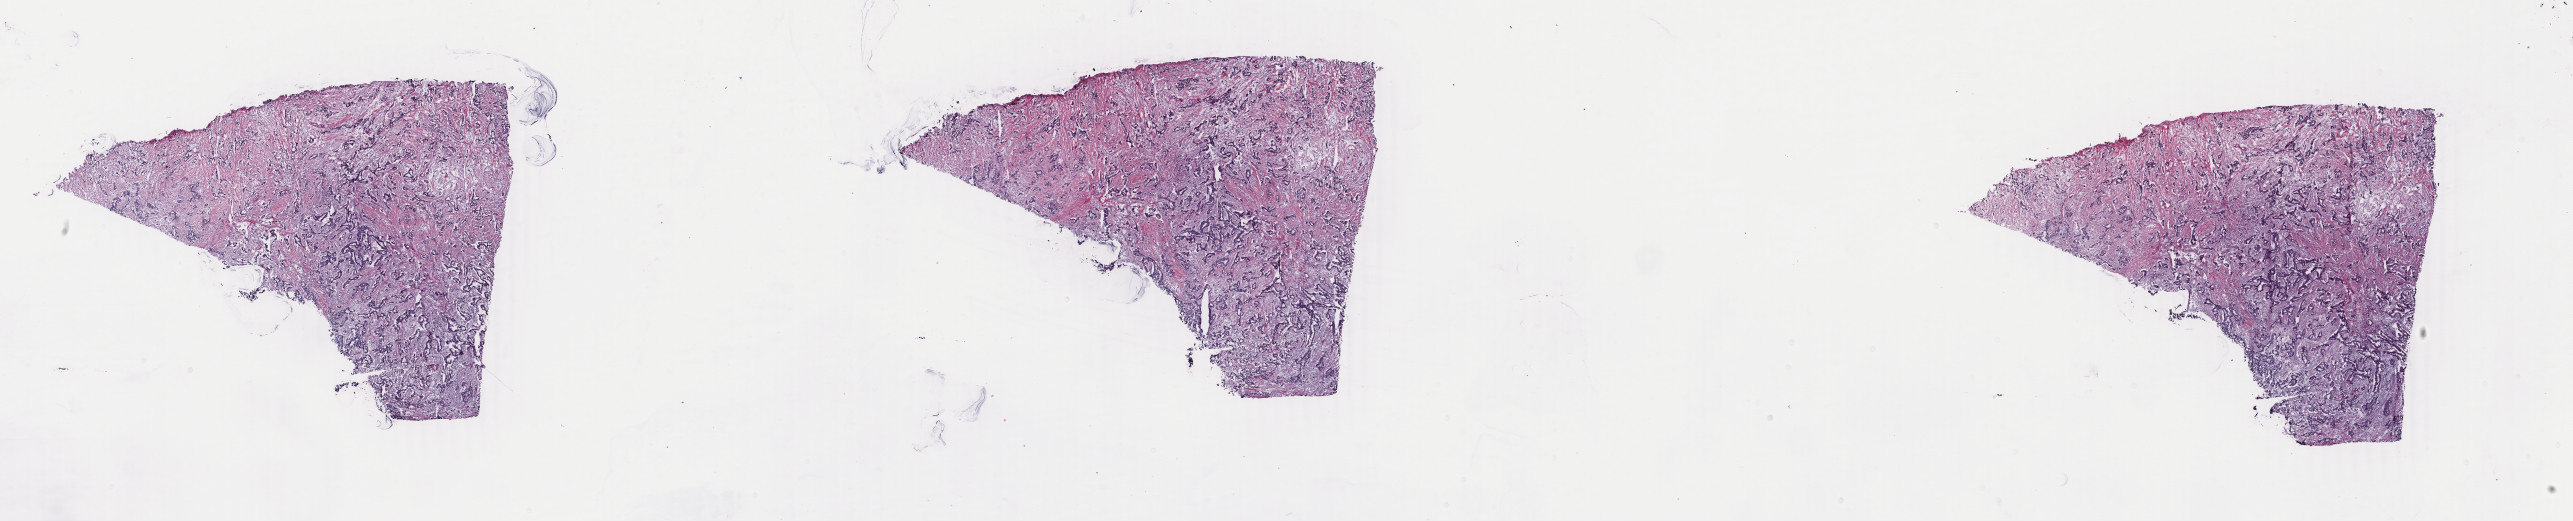
Hematoxylin and eosin (H&E) stained whole-slide image — whole scanned area (about 40.9 x 8.3 mm) shown as a low-resolution overview; frozen section; sample: primary tumour, breast. Female patient; age at initial diagnosis 71 years. Slide review estimates, as recorded: tumour cells 85%, tumour nuclei 85%, normal cells 0%, stromal cells 15%, necrosis 0%. Inflammatory infiltration, as recorded: lymphocyte infiltration 1%, monocyte infiltration 0%, neutrophil infiltration 0%.
* TNM: T2 N0 M0
* lymph nodes positive (case pathology): 0 of 14 examined
* pathologic diagnosis: Infiltrating duct carcinoma, NOS
* AJCC pathologic stage: IIA